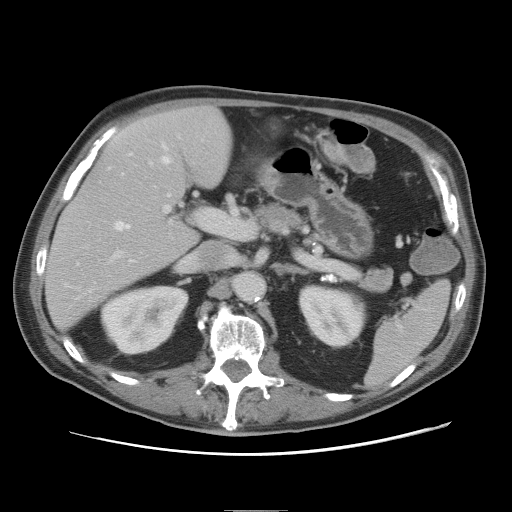
Contrast-enhanced abdominal CT, one axial slice. Position 41 of 89 along the scan axis. 120 kVp. Soft-tissue window (W 400 / L 40 HU). 5 mm slice thickness. 512 × 512 image matrix, field of view 375 × 375 mm. Male patient, age 69 years. Case-level facts recorded for this patient, not image findings: diagnosis: colorectal cancer liver metastases, imaged before liver resection; multiple liver metastases: no; largest metastasis: 8.5 cm; chemotherapy before resection: no.
Annotated regions visible in this slice (manually delineated by an expert):
- hepatic veins: bounding box (x1, y1, x2, y2) in pixels: (90, 144, 171, 291)
- liver: (46, 107, 232, 327)
- planned liver remnant (the part of the liver to remain after resection): (46, 107, 232, 327)
- portal vein (with intrahepatic branches): (113, 162, 224, 258)